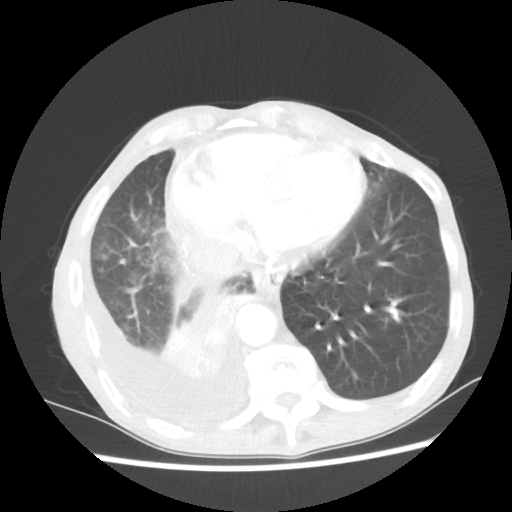
Chest CT, one axial slice. Slice 17 of 60 in the series (ordered by position). Reconstruction kernel STANDARD. 80 kVp. Lung window (W 1500 / L -600 HU). 5 mm slice thickness. 512 × 512 image matrix, field of view 335 × 335 mm. Male patient, age 76 years. Case-level facts recorded for this patient, not image findings: clinical TNM (as recorded): T3 N3 M1a.
Outlined on this slice (bounding box drawn by a radiologist):
- lung tumour (recorded histology: squamous cell carcinoma): box from (x=161, y=284) to (x=256, y=382) px